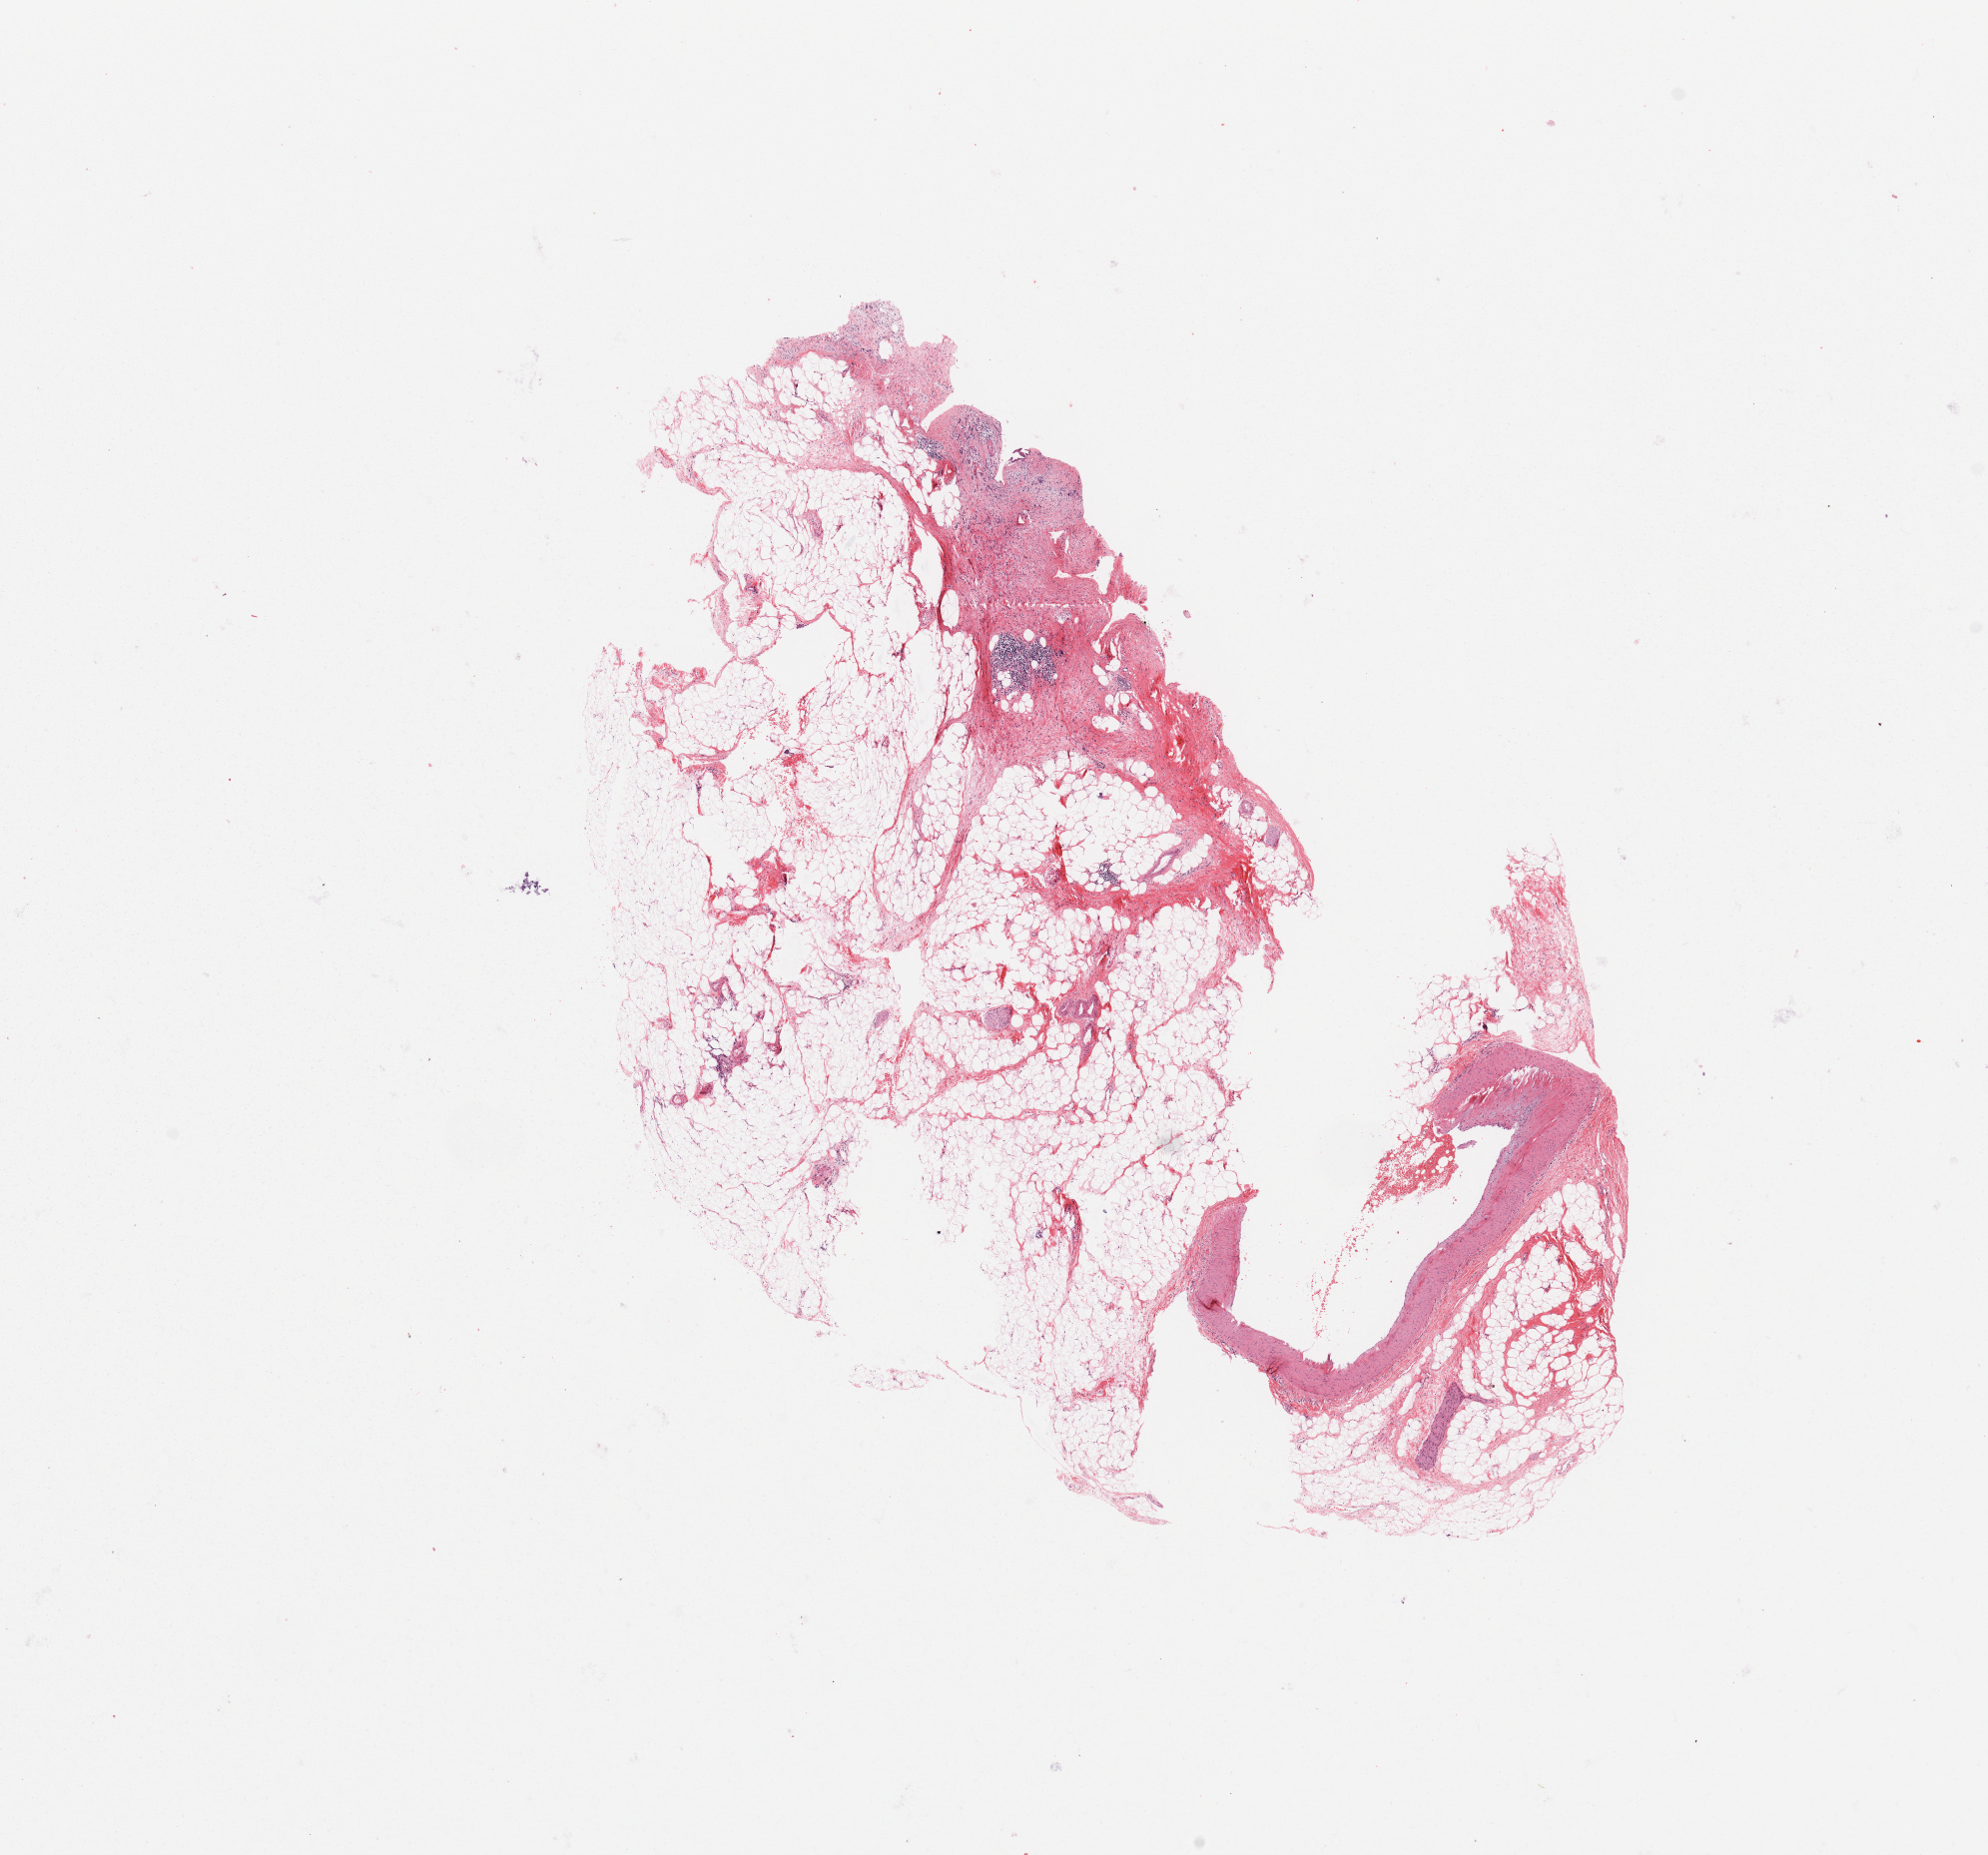
Digitized H&E tissue section (whole slide) — a low-resolution overview of the entire scanned area, about 15.8 x 14.7 mm. Normal (non-tumour) tissue sample, sampled site: pancreas. Patient: male, age 69 years.
• this section: normal (non-tumour) tissue from the same patient
• patient diagnosis: Infiltrating duct carcinoma, NOS